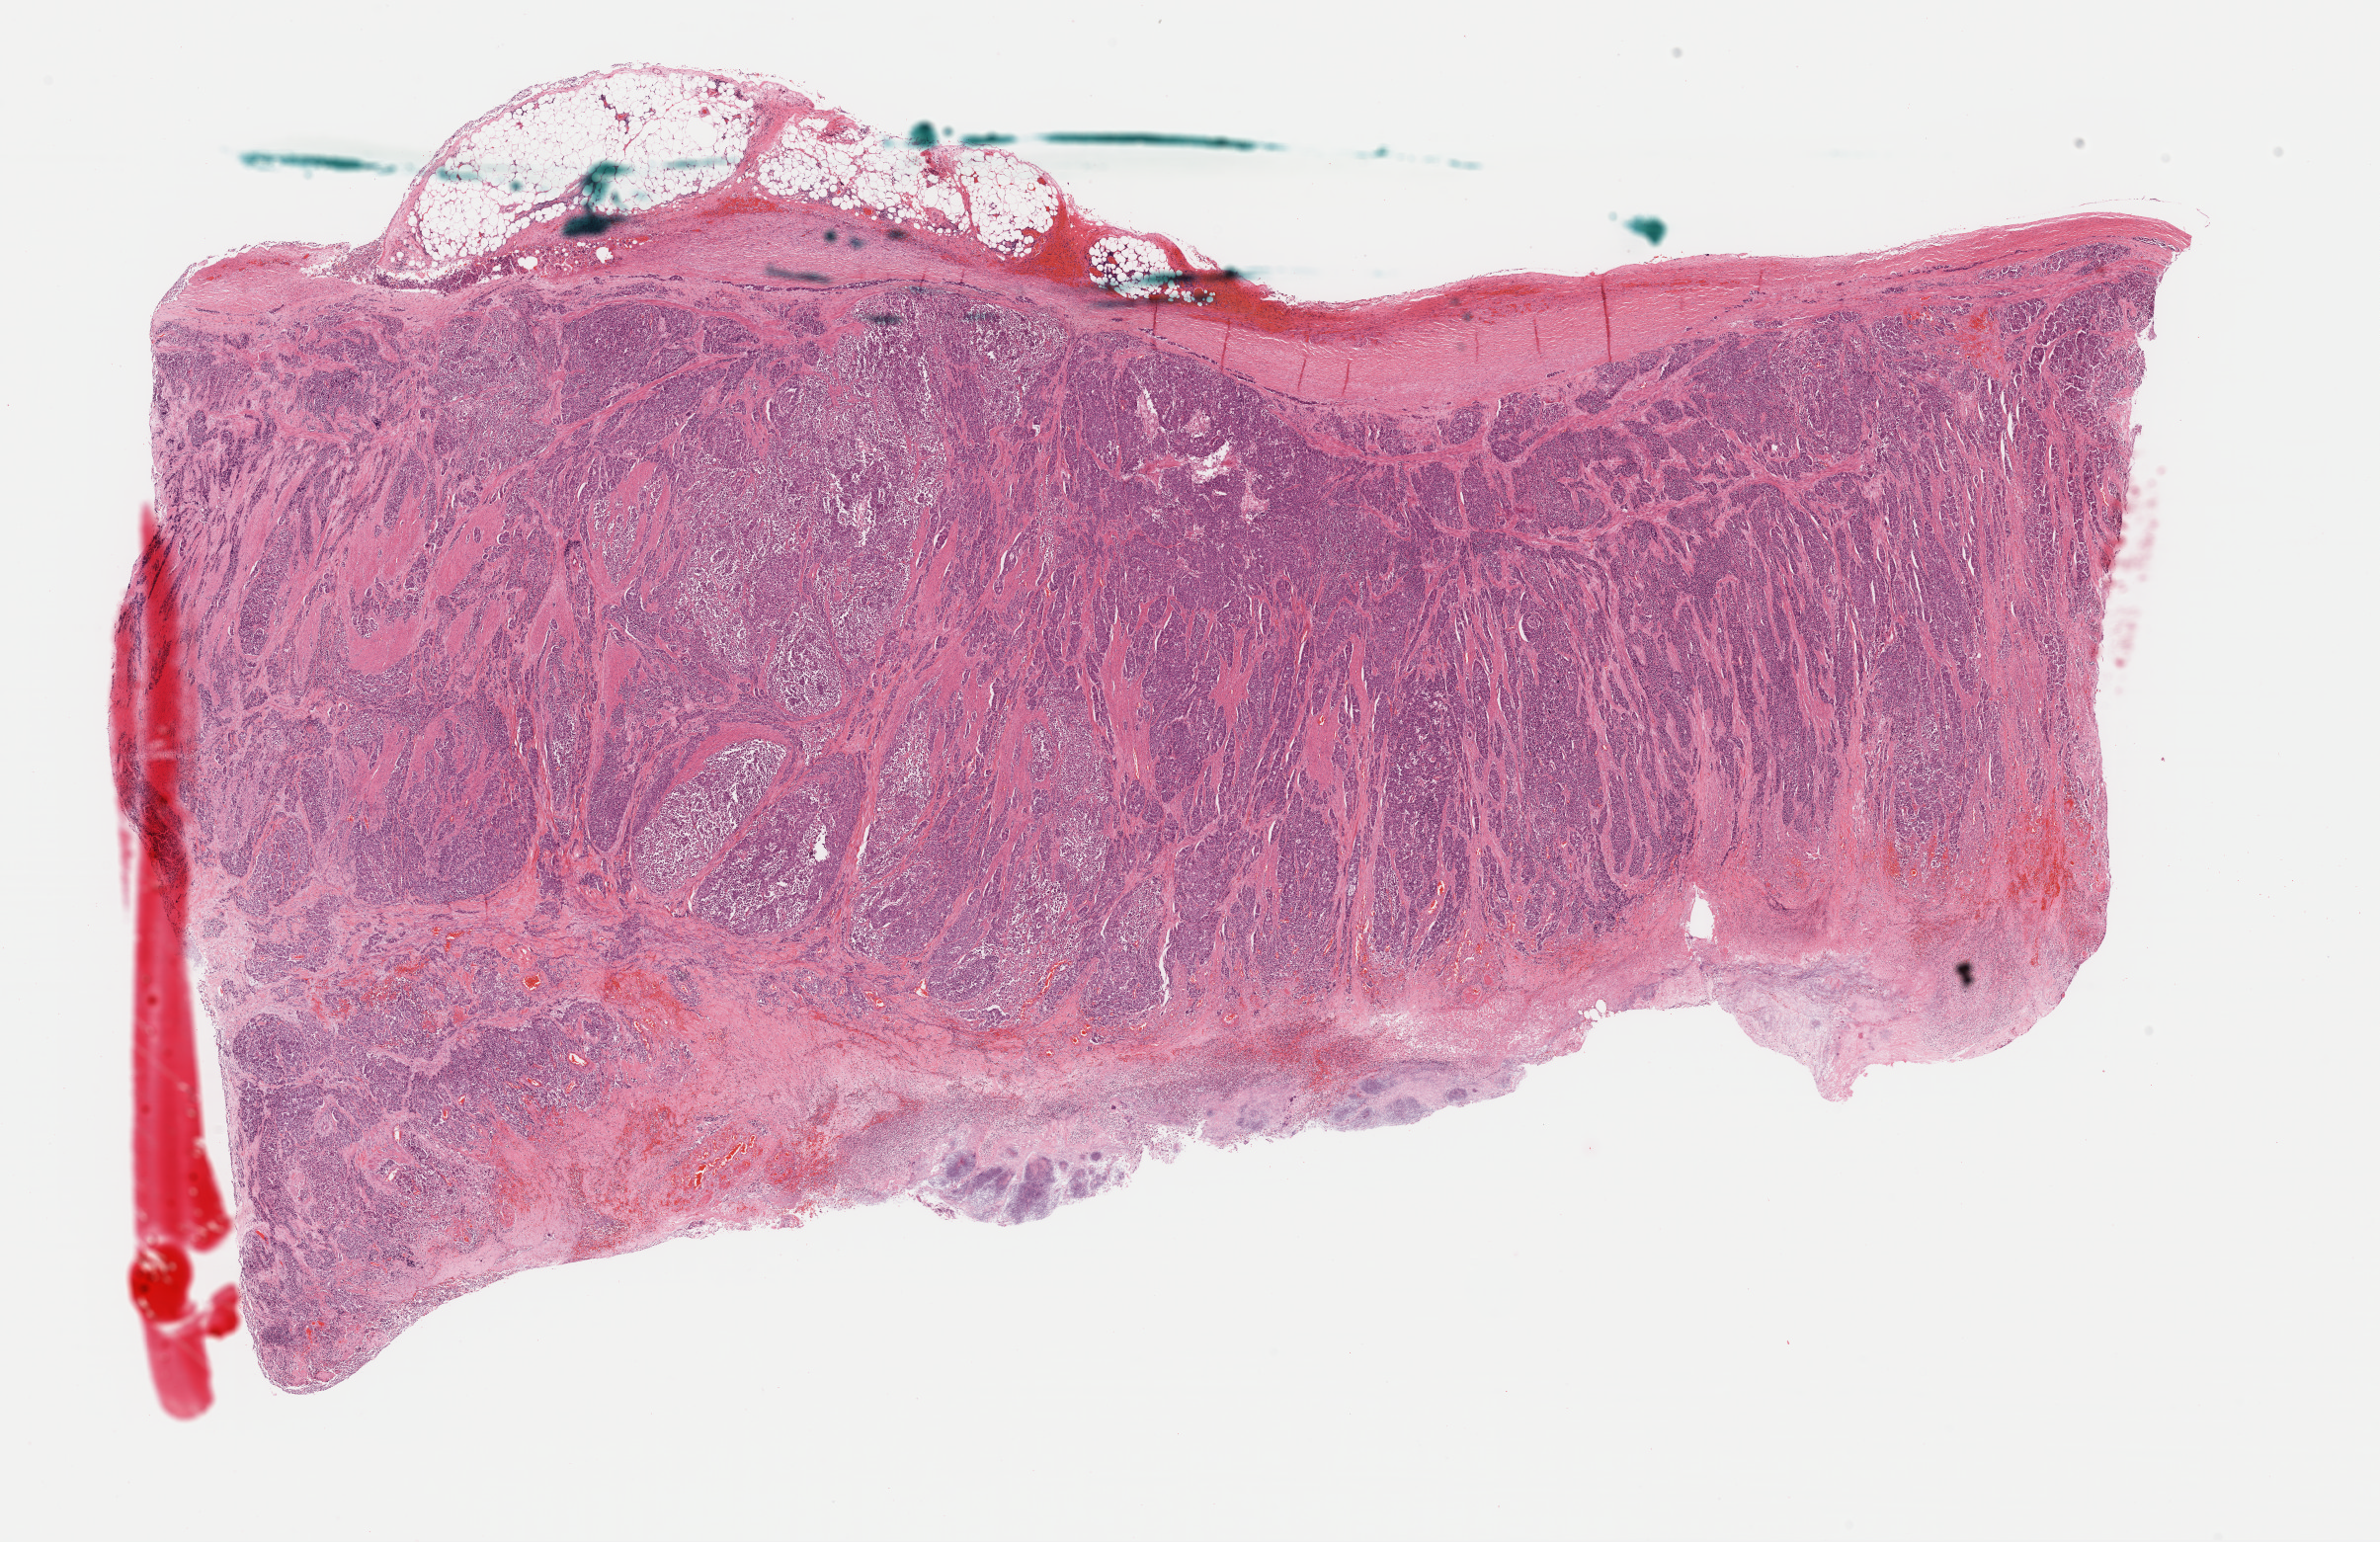
Digitized Hematoxylin and eosin (H&E) stained tissue section (whole slide) — shown as a low-resolution overview of the whole scanned area (about 19.0 x 12.3 mm, acquisition: 40x scan), formalin-fixed paraffin-embedded (FFPE) diagnostic section, primary tumour sample from the stomach. Female patient; age at initial diagnosis 70 years. Histologic grade: G3 (poorly differentiated).
• pathologic diagnosis: Adenocarcinoma, NOS (fundus of stomach)
• AJCC pathologic stage: IIIC
• lymph nodes positive (case pathology): 8 of 8 examined